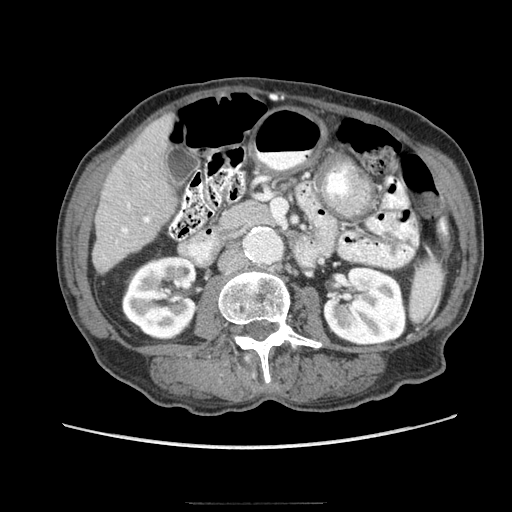
Contrast-enhanced abdominal CT (liver protocol), one axial slice. Slice 26 of 83 in the series (ordered by position). 140 kVp. Soft-tissue window (W 400 / L 40 HU). 2.5 mm slice thickness. 512 × 512 image matrix, field of view 360 × 360 mm. From the clinical record (not read from this slice): diagnosis: hepatocellular carcinoma (patient treated with transarterial chemoembolisation; whether this scan precedes or follows treatment is not stated here); TNM stage (as recorded): Stage-I; Child-Pugh class: A; tumour differentiation: moderately differentiated; tumour nodularity: uninodular.
Annotated regions visible in this slice (semi-automatic segmentation, software-assisted and operator-edited):
- liver parenchyma outside the tumour (the mass and vessels are separate outlines, so this box may not span the whole liver): box from (x=92, y=114) to (x=176, y=272) px
- liver vessels: (x=122, y=203)–(x=149, y=233)